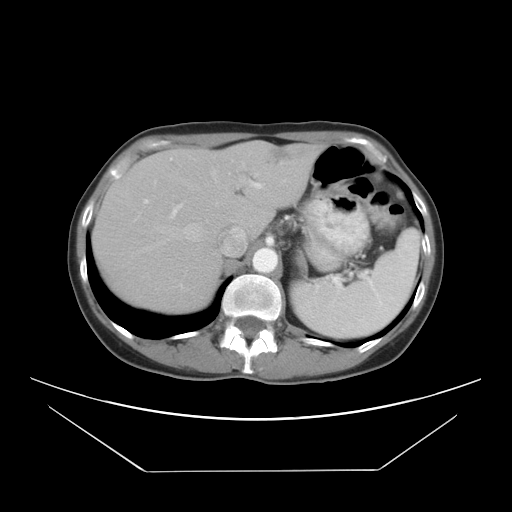
Contrast-enhanced abdominal CT, one axial slice; position 21 of 30 along the scan axis; reconstruction kernel STANDARD; 120 kVp; intravenous contrast given; soft-tissue window (W 400 / L 40 HU); 7.5 mm slice thickness; 512 × 512 image matrix, field of view 412 × 412 mm. Female patient, age 54 years. Case-level facts recorded for this patient, not image findings: diagnosis: colorectal cancer liver metastases, imaged before liver resection; multiple liver metastases: yes; largest metastasis: 2.5 cm; disease in both lobes: yes.
Outlined on this slice (manually delineated by an expert):
- hepatic veins: bounding box <139,170,217,252> (left, top, right, bottom; pixels)
- liver: <94,143,319,312>
- planned liver remnant (the part of the liver to remain after resection): <94,147,269,313>
- portal vein (with intrahepatic branches): <155,182,262,234>
- liver metastasis: <268,150,293,168>